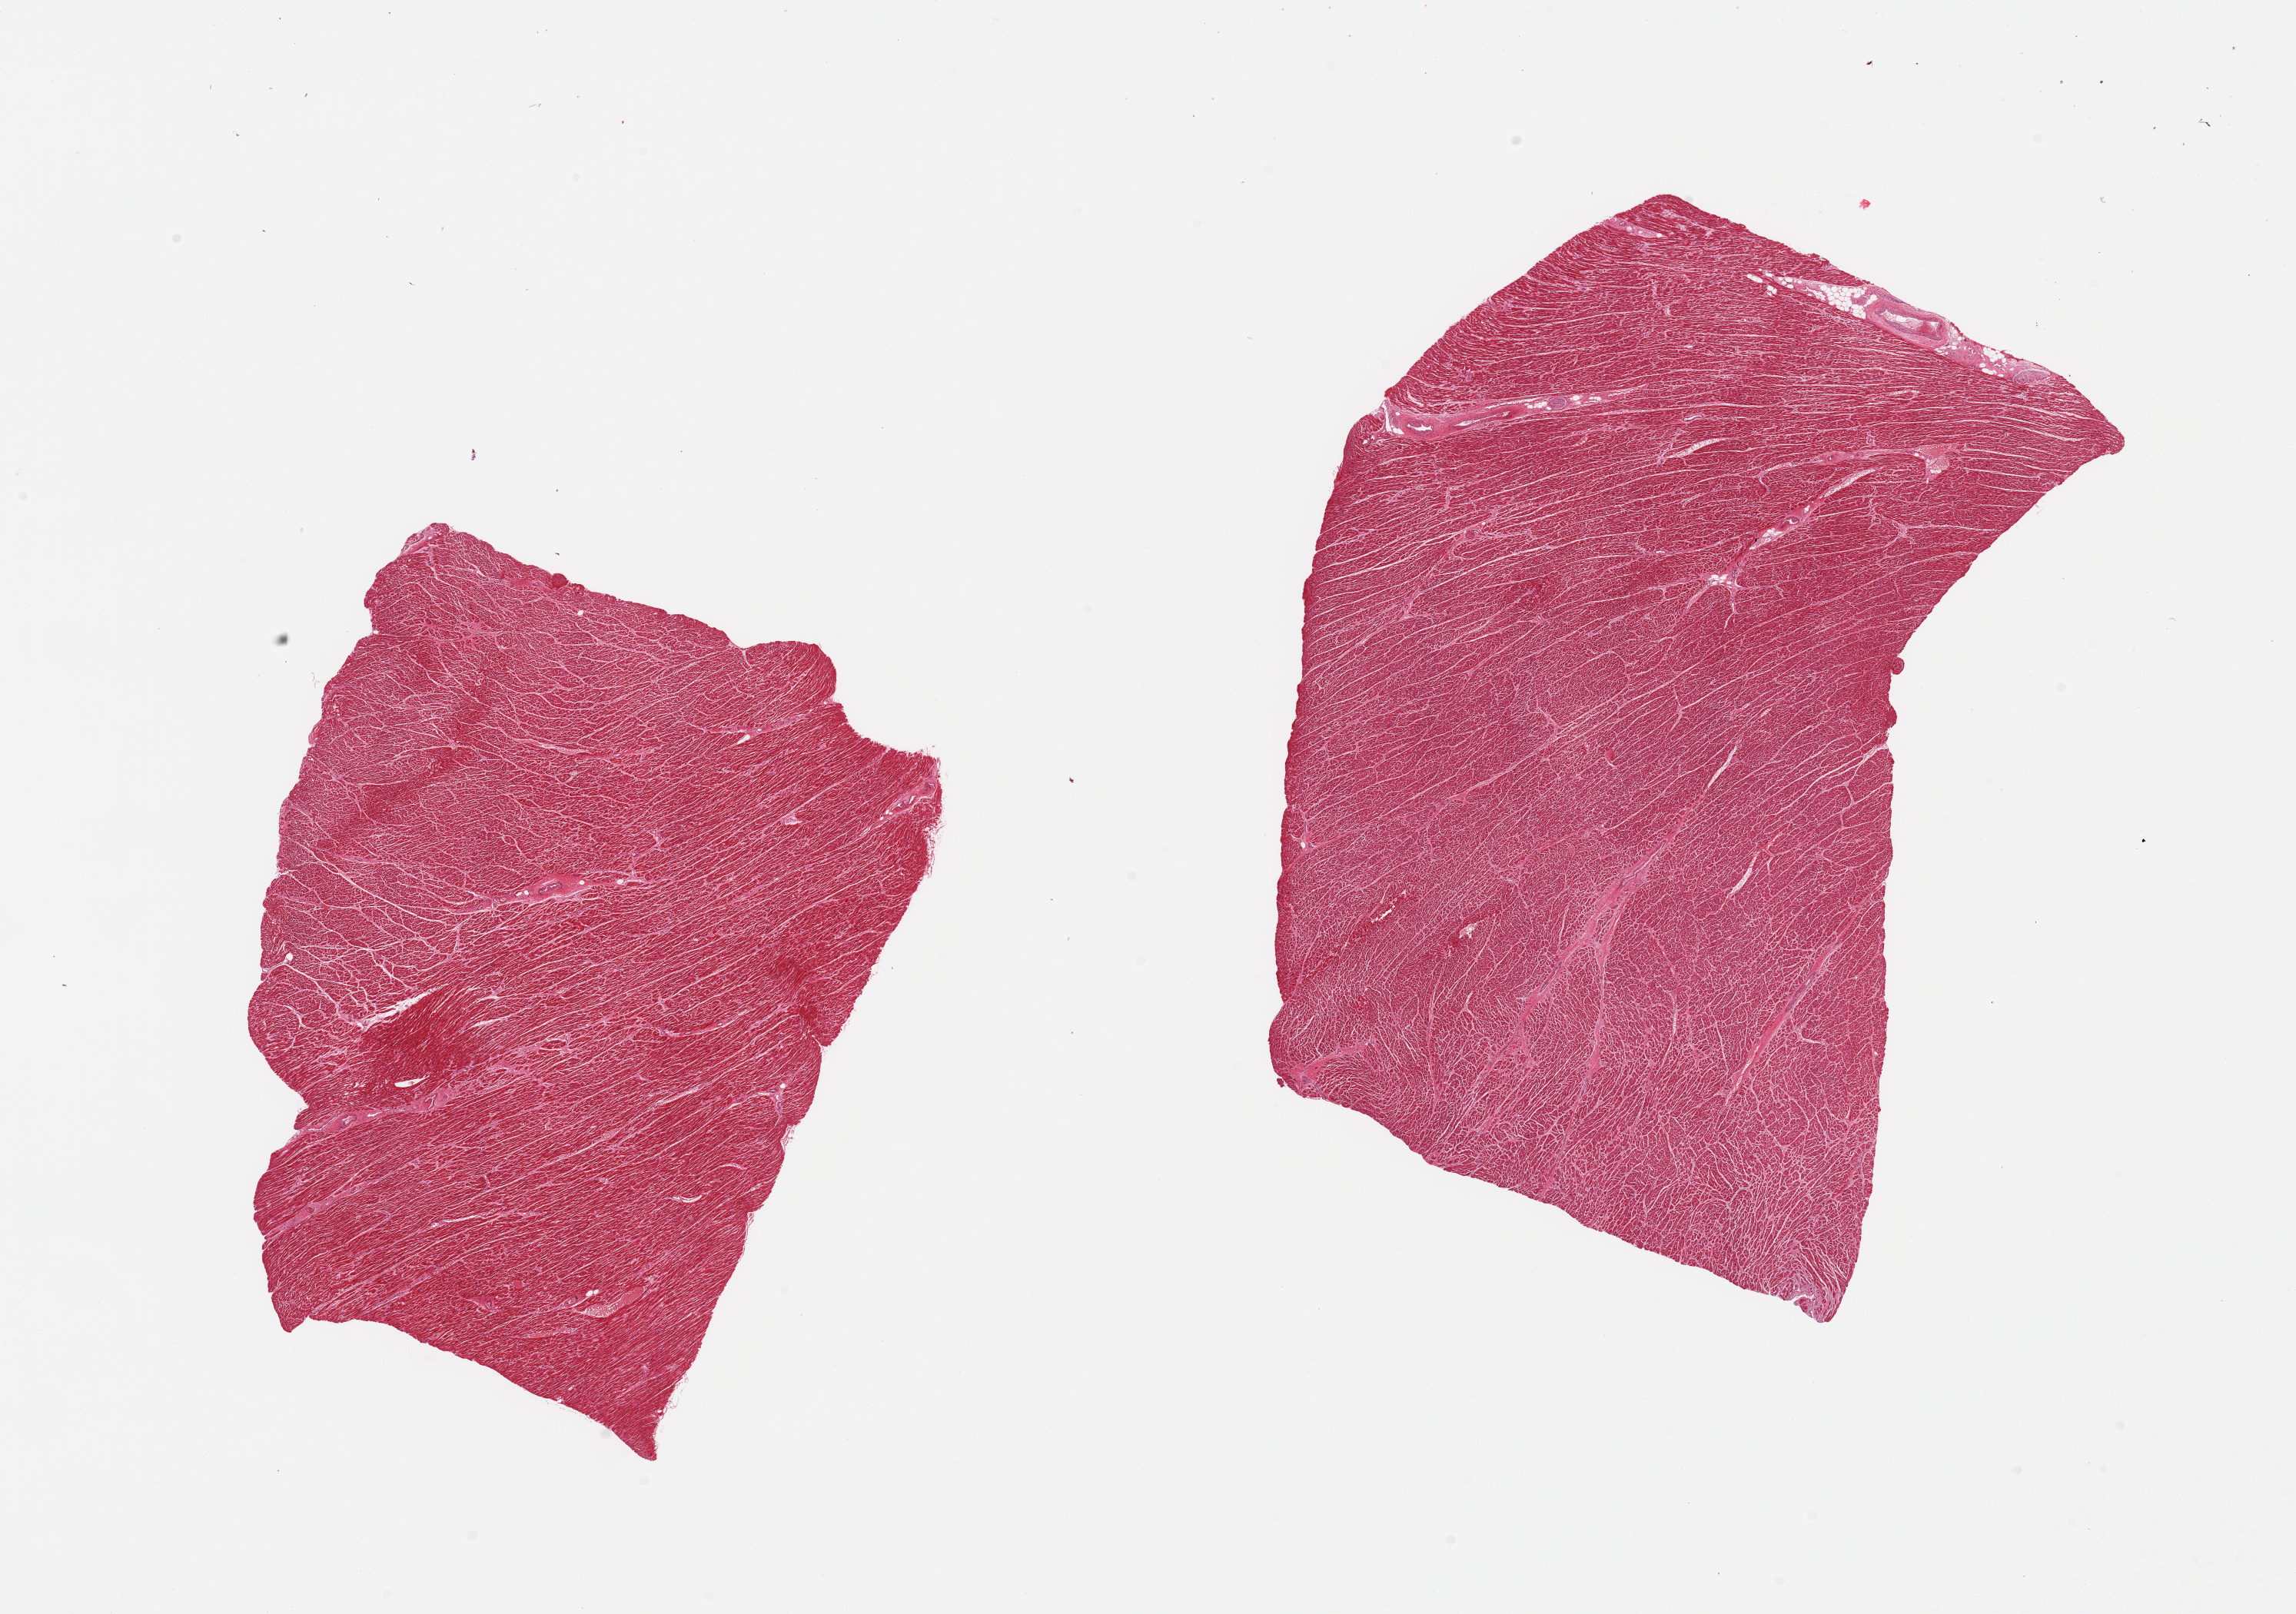
Whole-slide image, hematoxylin and eosin (H&E) stain — a low-resolution overview of the entire scanned area, about 23.6 x 16.6 mm; PAXgene-fixed paraffin-embedded (PFPE) section; sampled site (target tissue): heart; donor tissue sample. Donor sex: male.
- reviewer comment on this tissue sample: 2 pieces, trace interstitial fibrosis/chronic ischemic changes